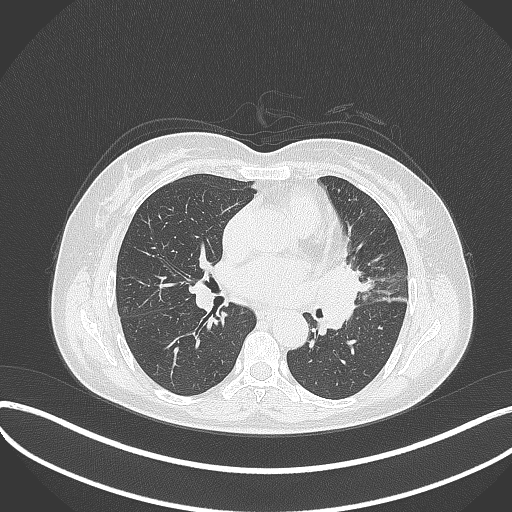
Chest CT, one axial slice; position 181 of 373 along the scan axis; reconstruction kernel B70f; 120 kVp; lung window (W 1500 / L -600 HU); 512 × 512 image matrix, field of view 400 × 400 mm. Female patient, age 54 years. From the clinical record (not read from this slice): clinical TNM (as recorded): T2a N1 M0.
Annotated regions visible in this slice (rectangle marked by the reading radiologist):
- lung tumour (recorded histology: small cell carcinoma): box from (x=315, y=258) to (x=364, y=337) px